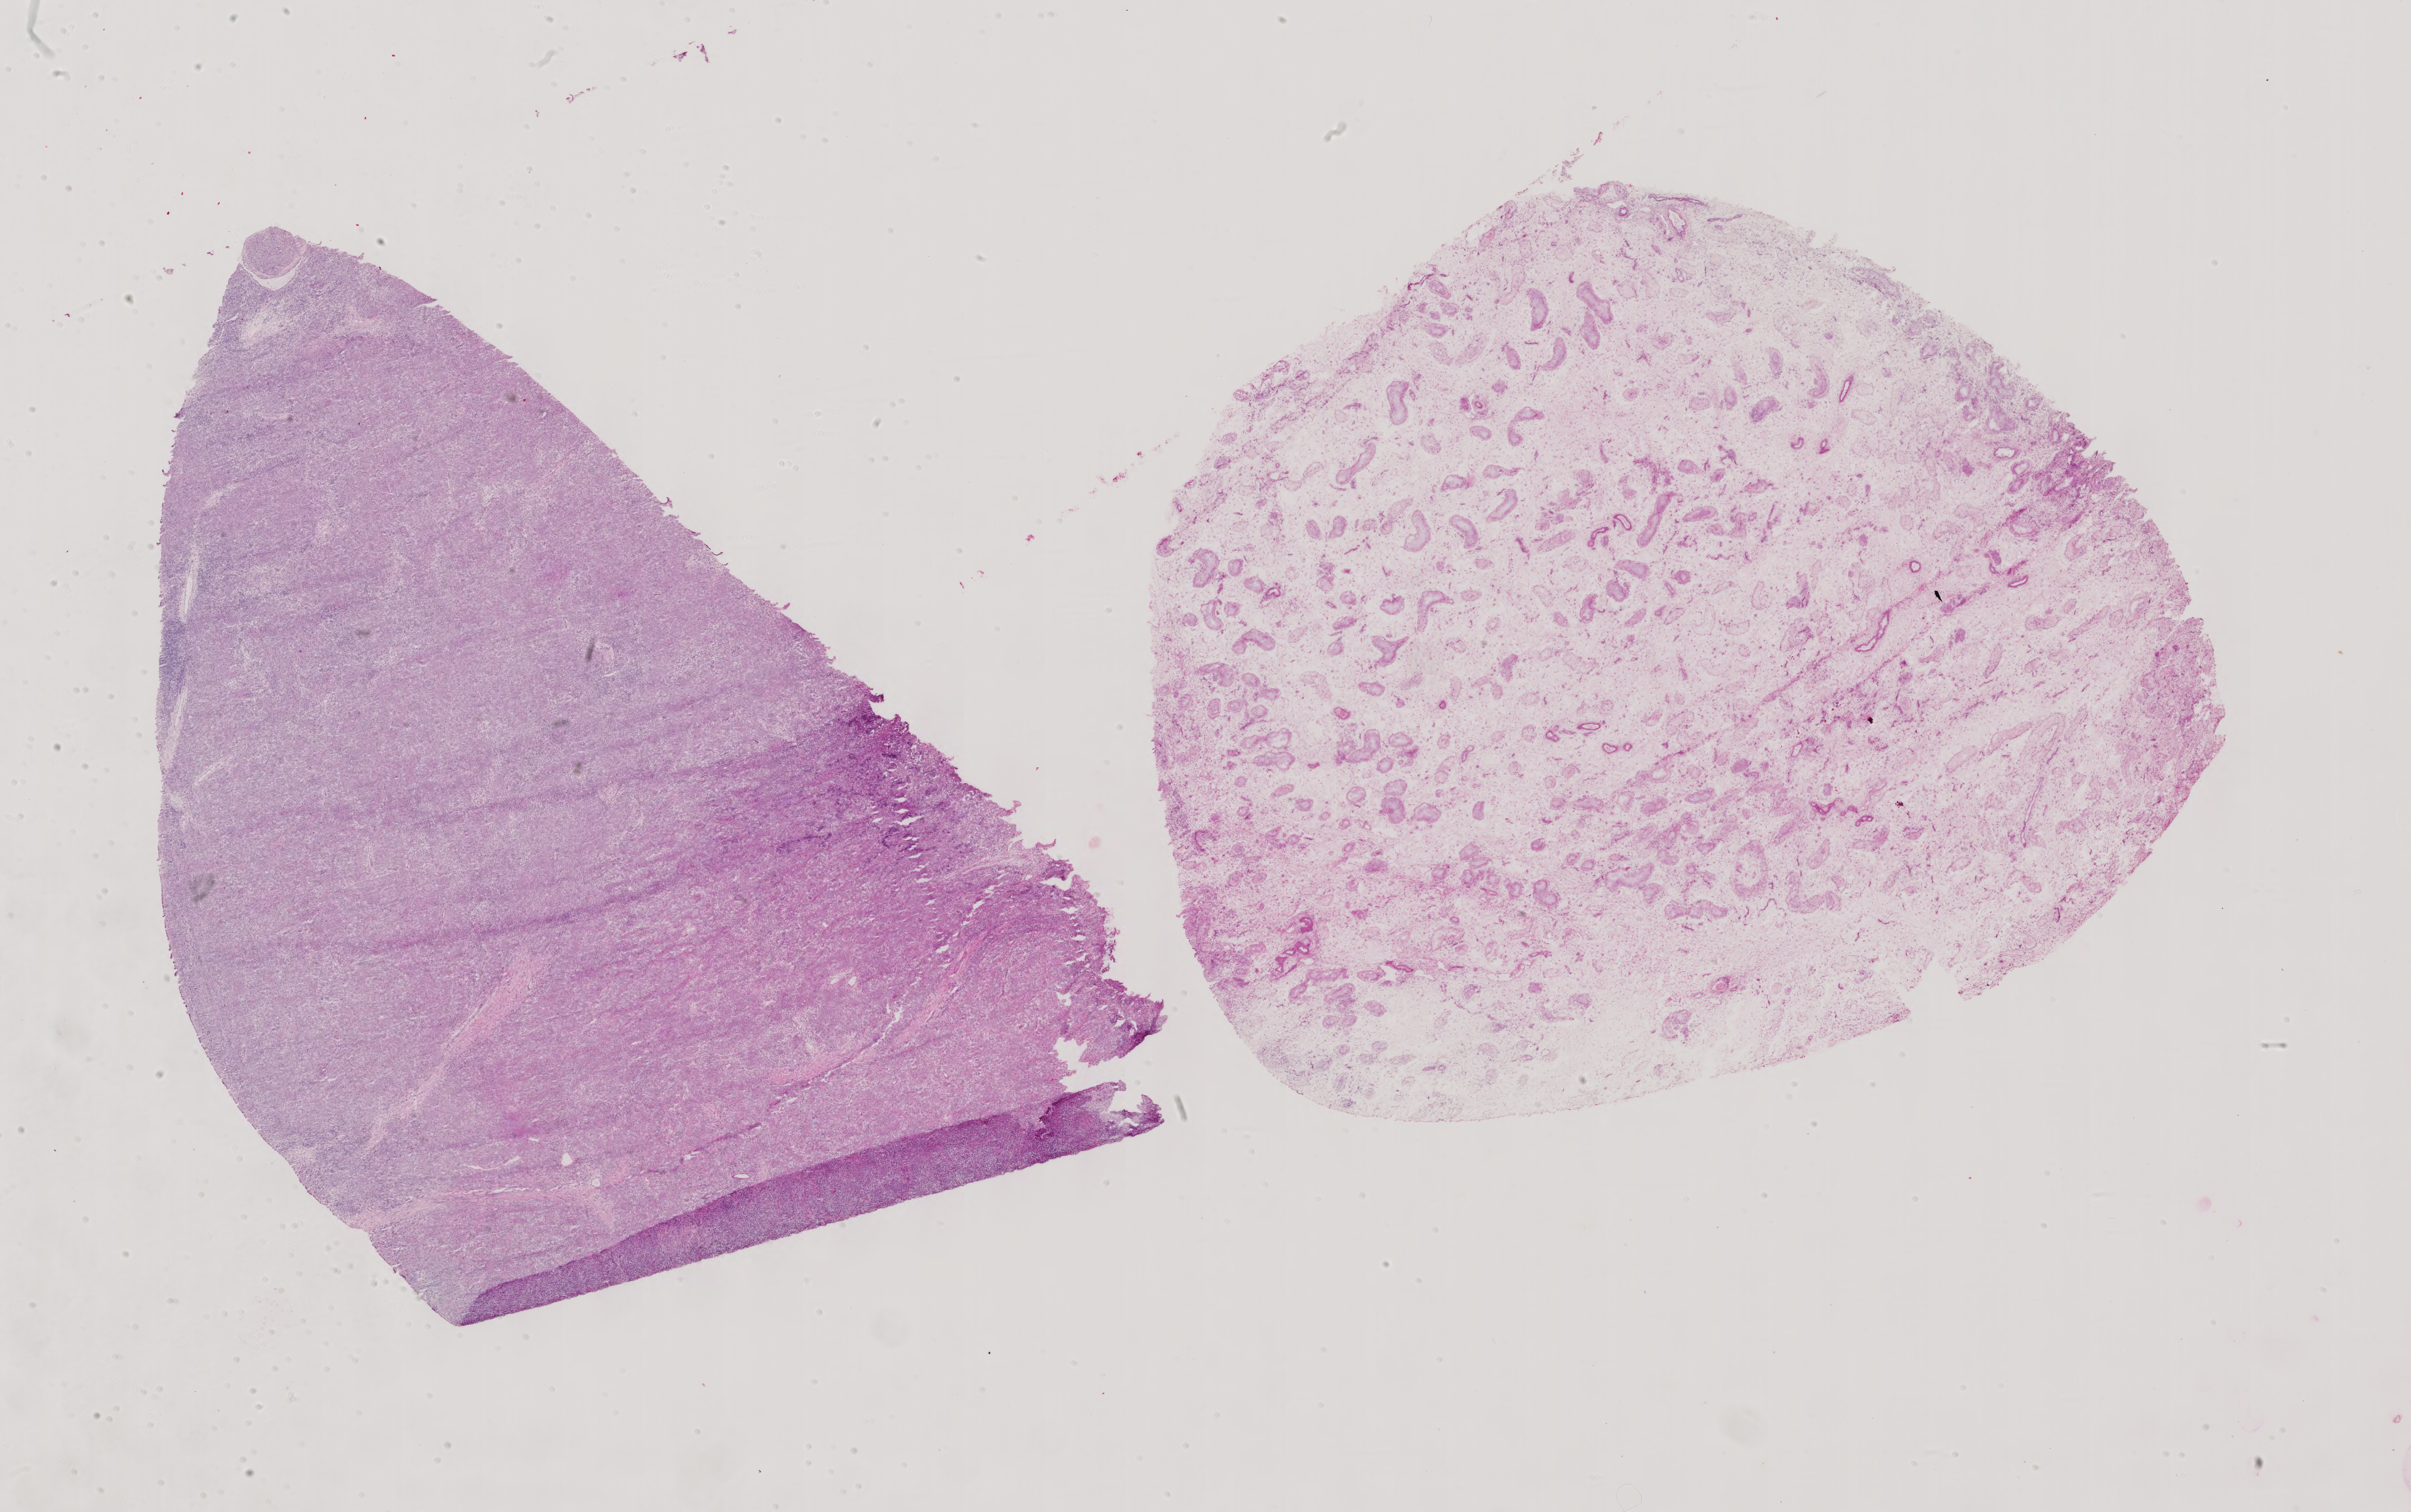
Hematoxylin and eosin (H&E) stained whole-slide image, shown as a low-resolution overview of the whole scanned area (about 28.0 x 17.5 mm, slide scanned at 40x), FFPE section, sample: primary tumour, testis. Male patient; age at initial diagnosis 48 years.
AJCC pathologic stage: IB (6th edition). Histologic diagnosis: Seminoma, NOS. Laterality: left.